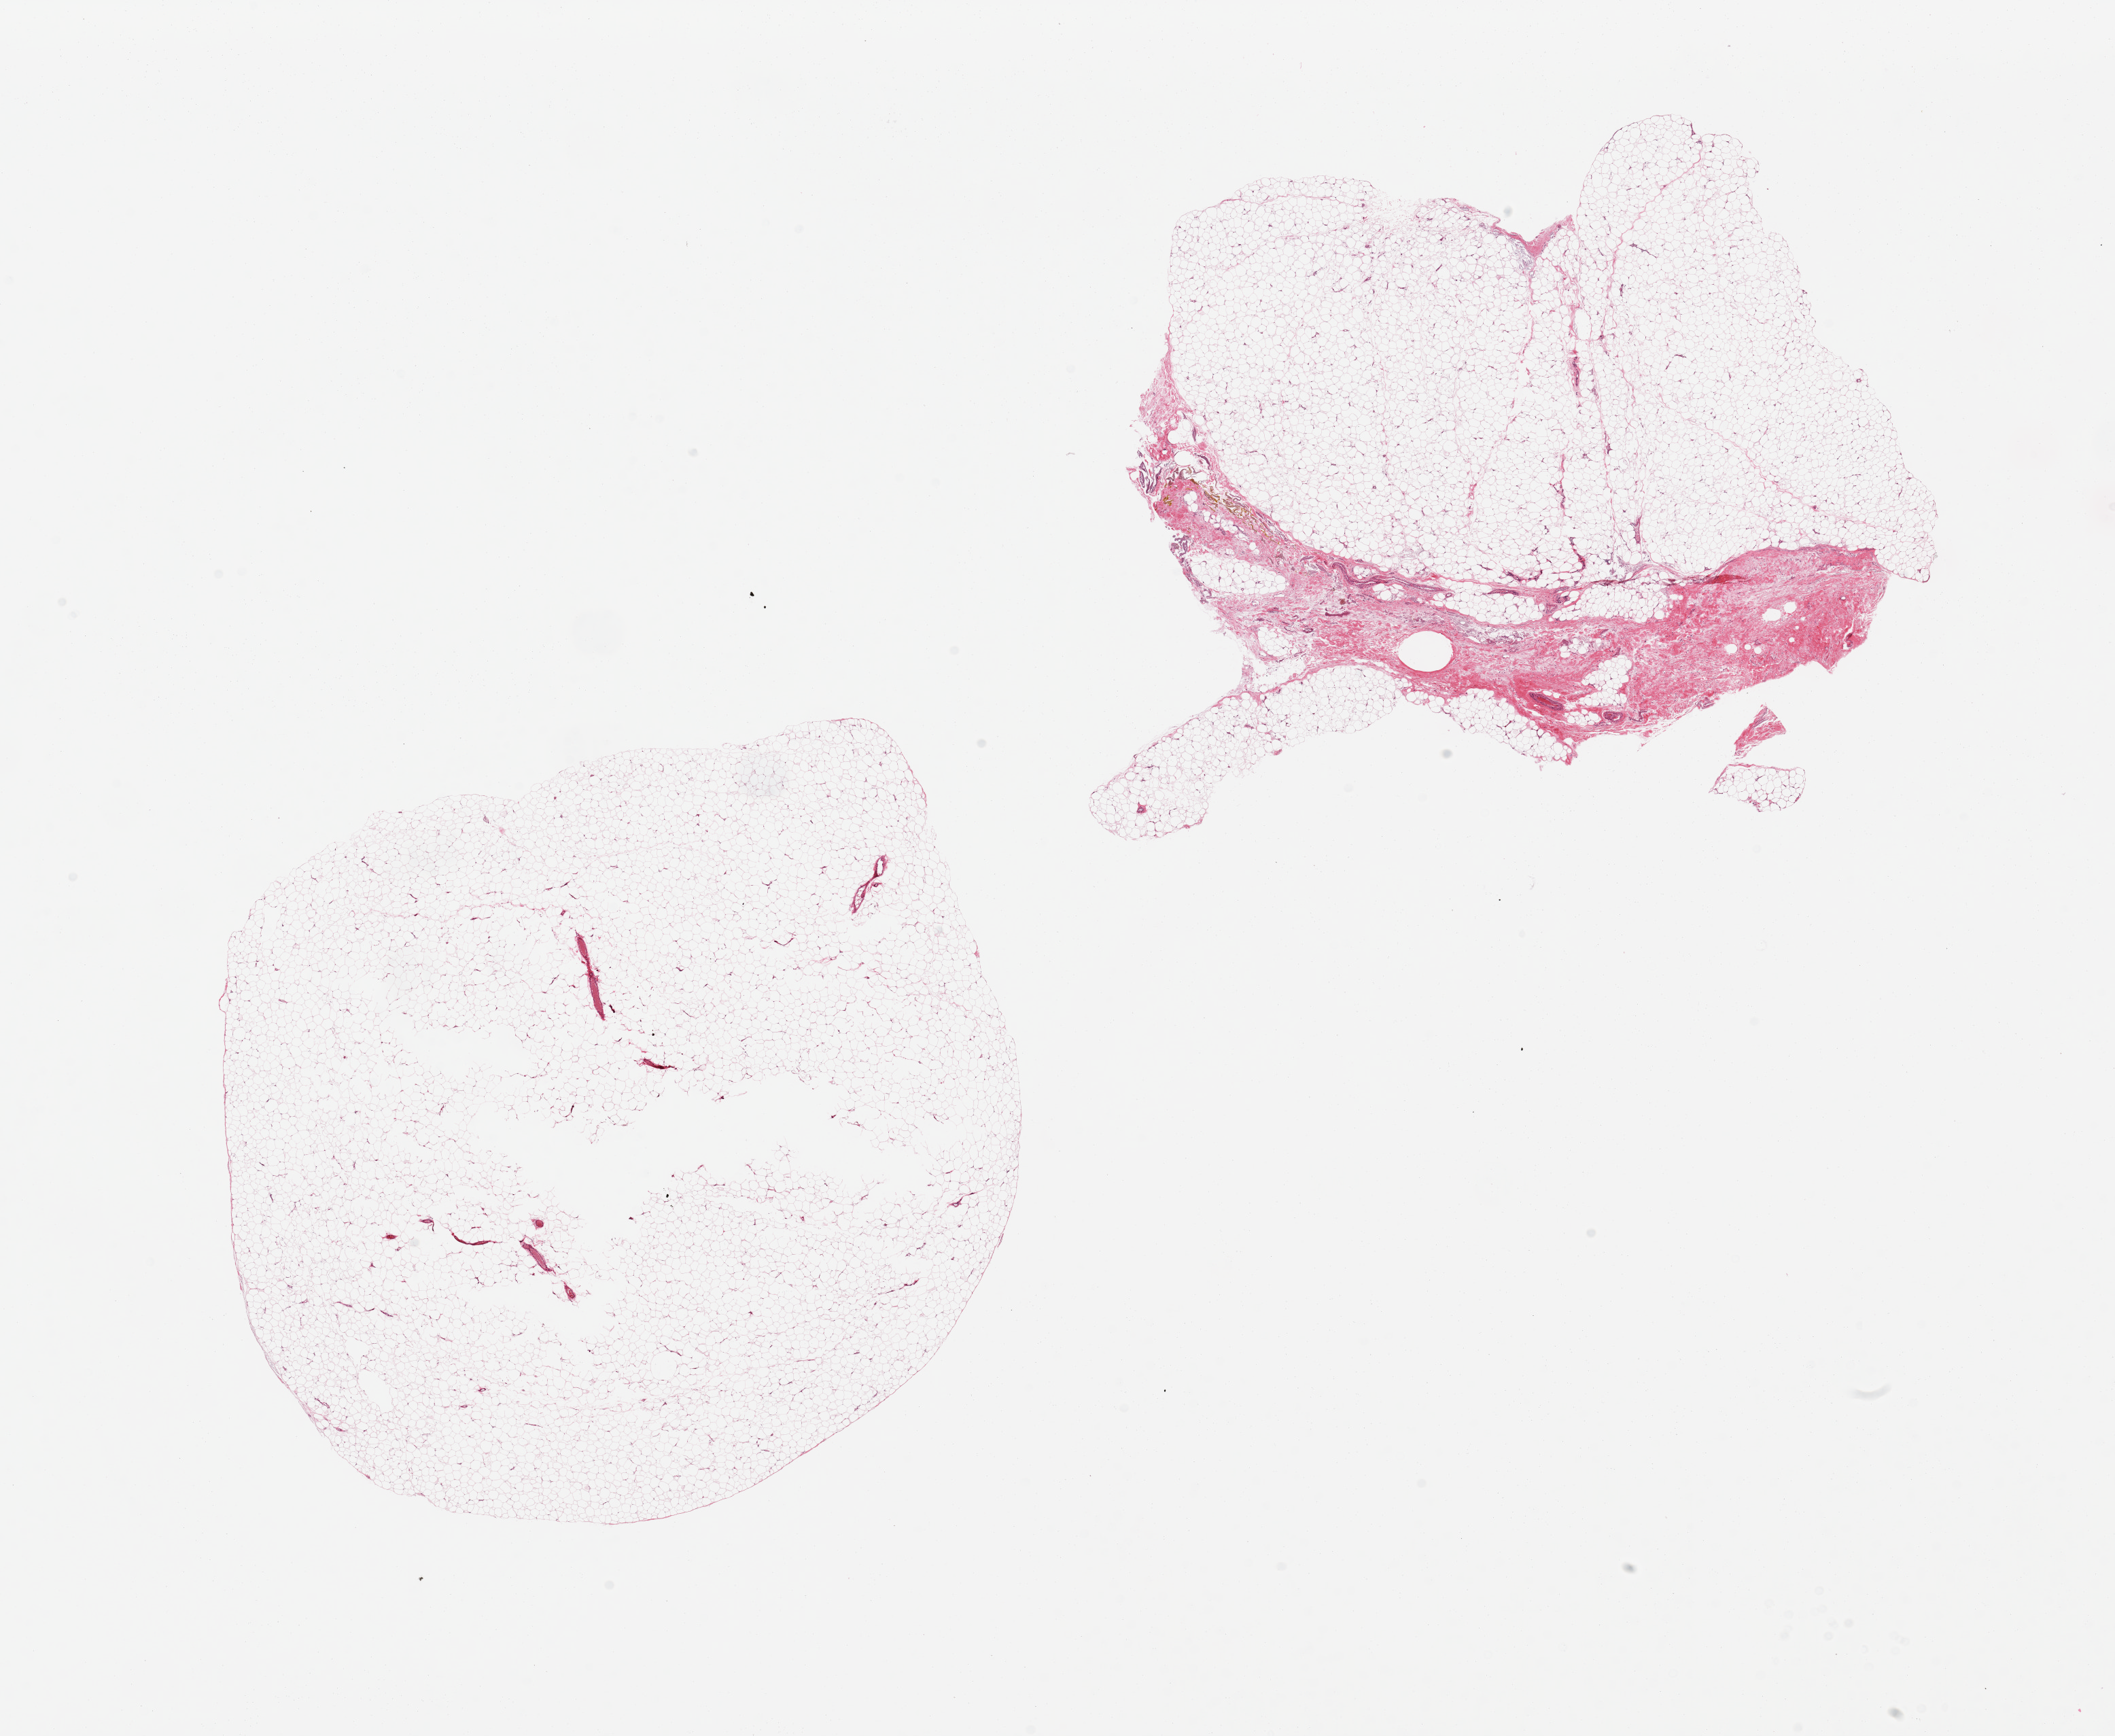
H&E whole-slide image, shown as a low-resolution overview of the whole scanned area (about 24.6 x 20.2 mm, acquisition: 20x scan); PAXgene-fixed paraffin-embedded (PFPE) section; target tissue: adipose tissue; tissue donor sample. Male donor.
Review note (as recorded): 2 pieces,j ~10% fibrofascial tissue.